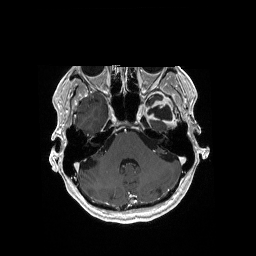
Brain MRI from a brain-tumour surgery series, one axial slice; position 132 of 176 along the scan axis; T1-weighted post-contrast; 1 mm slice thickness; 256 × 256 image matrix, field of view 256 × 256 mm. From the clinical record (not read from this slice): histopathology: Glioblastoma; WHO grade: 4; IDH mutation: no; tumour location: Left Medial Temporal.
Structures marked on this image (outlined manually by an expert reader):
- previous resection cavity: box from (x=148, y=105) to (x=172, y=120) px